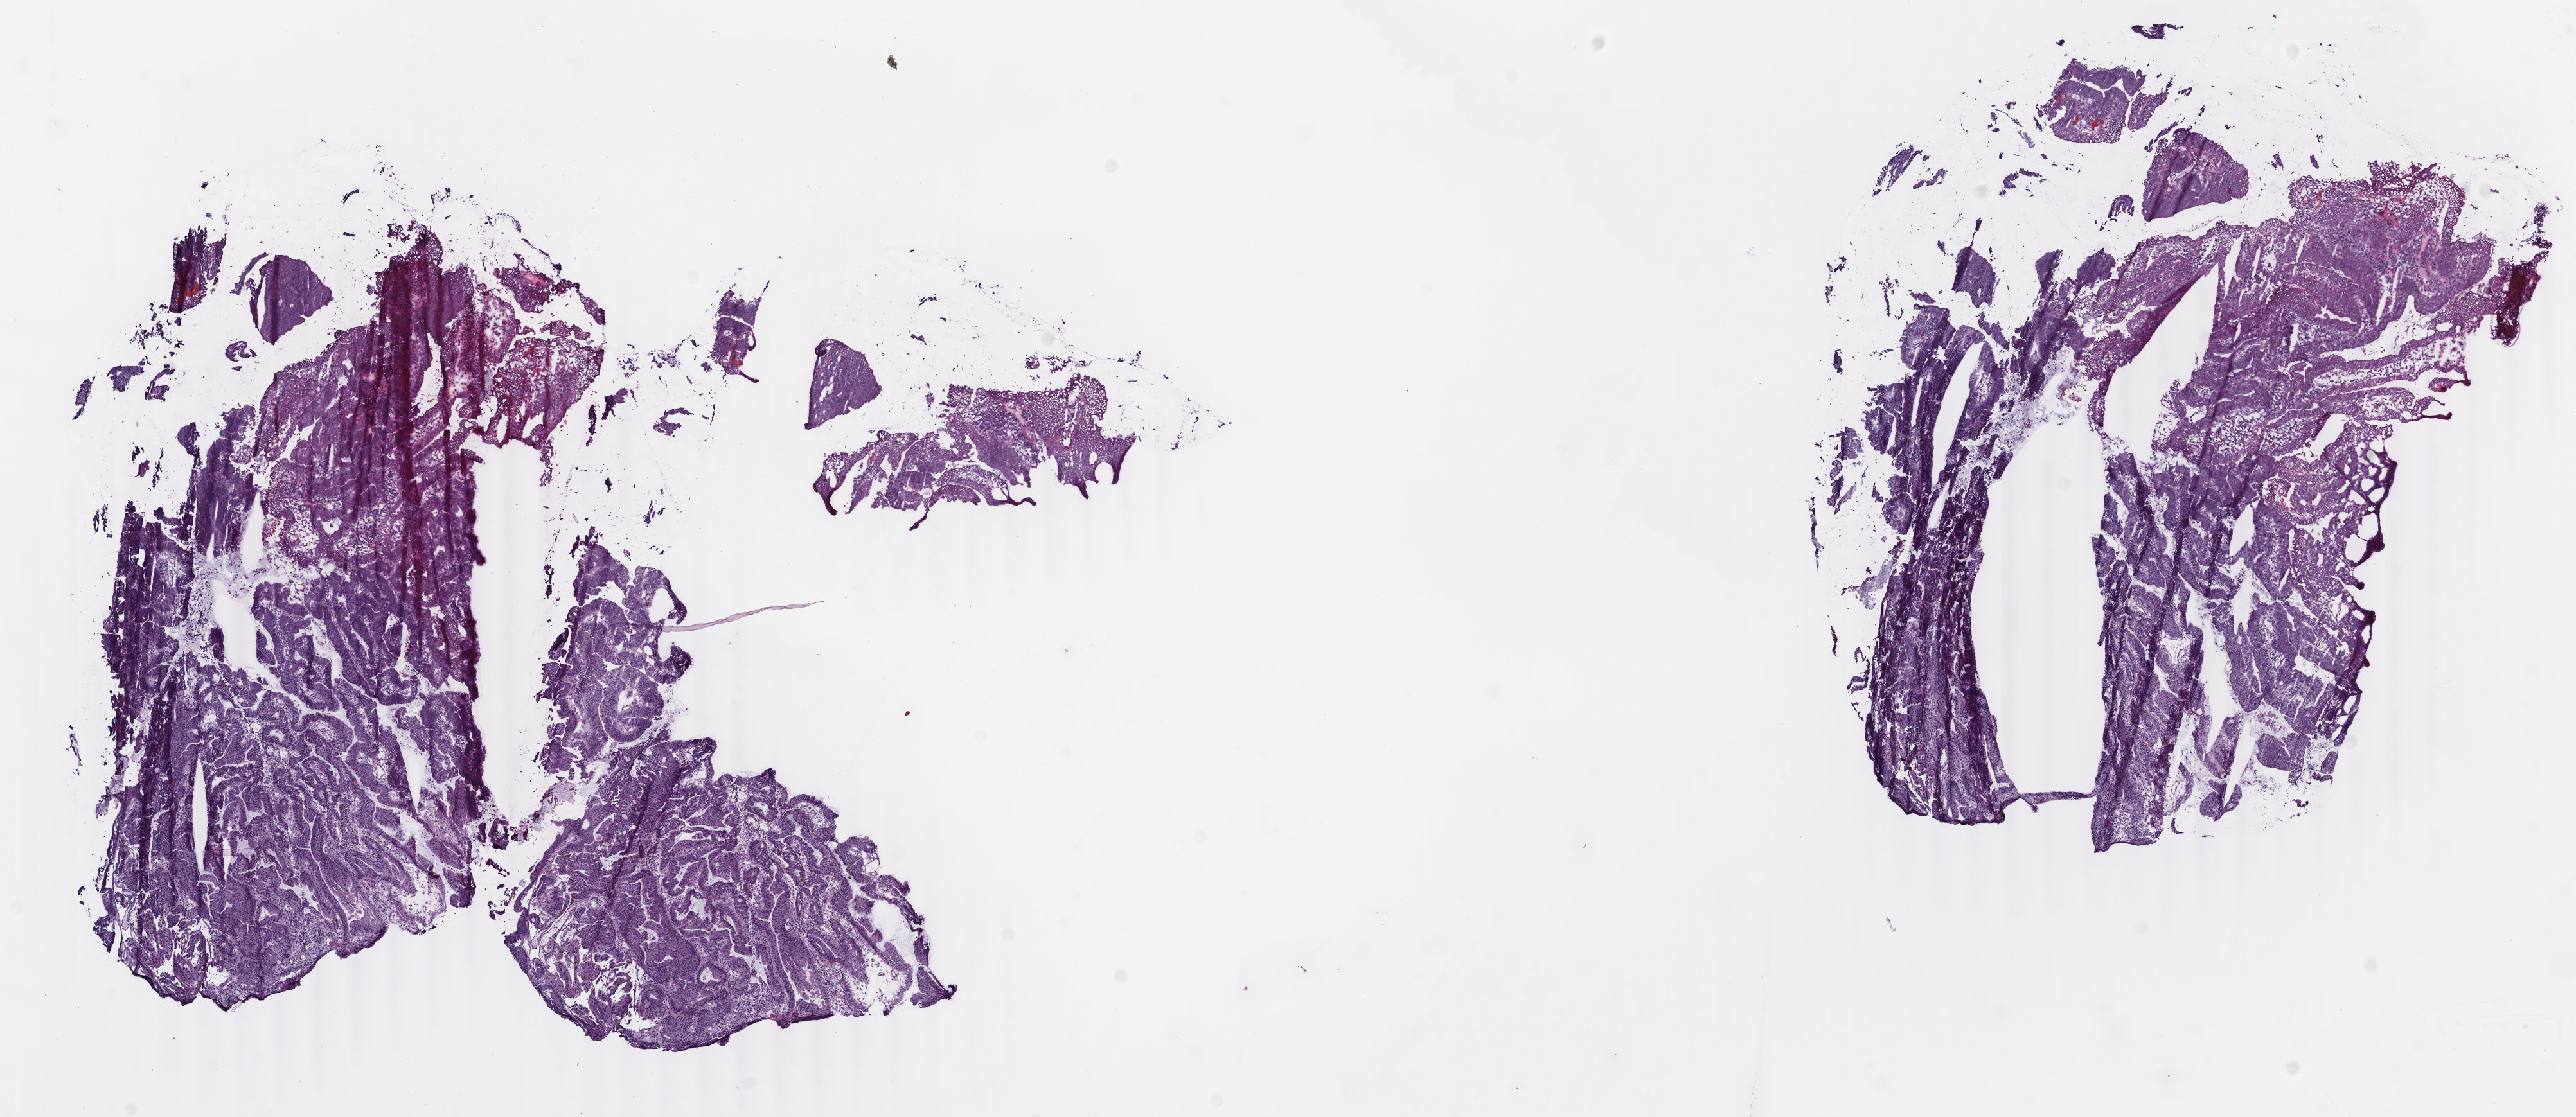
Digitized H&E tissue section (whole slide) — a low-resolution overview of the entire scanned area, about 15.9 x 6.9 mm. Frozen section. Rectum, primary tumour sample. Patient: male, age at initial diagnosis 67 years. Slide review estimates, as recorded: tumour cells 90%, tumour nuclei 85%, normal cells 0%, stromal cells 8%, necrosis 2%. Infiltration values recorded for this section: lymphocyte infiltration 8%, monocyte infiltration 1%, neutrophil infiltration 2%.
* diagnosis: Adenocarcinoma, NOS
* lymph nodes positive (case pathology): 0 of 12 examined
* AJCC pathologic stage: II (5th edition)